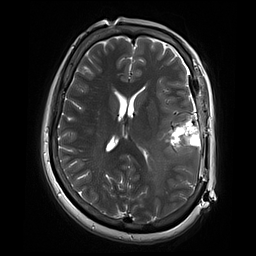
Brain MRI from a brain-tumour surgery series, one axial slice; slice 33 of 70 in the series (ordered by position); 2 mm slice thickness; 256 × 256 image matrix, field of view 220 × 220 mm. From the clinical record (not read from this slice): histopathology: Glioblastoma; WHO grade: 4; IDH mutation: no.
Outlined on this slice (manually delineated by an expert):
- residual tumour: bounding box (x1, y1, x2, y2) in pixels: (158, 116, 174, 138)